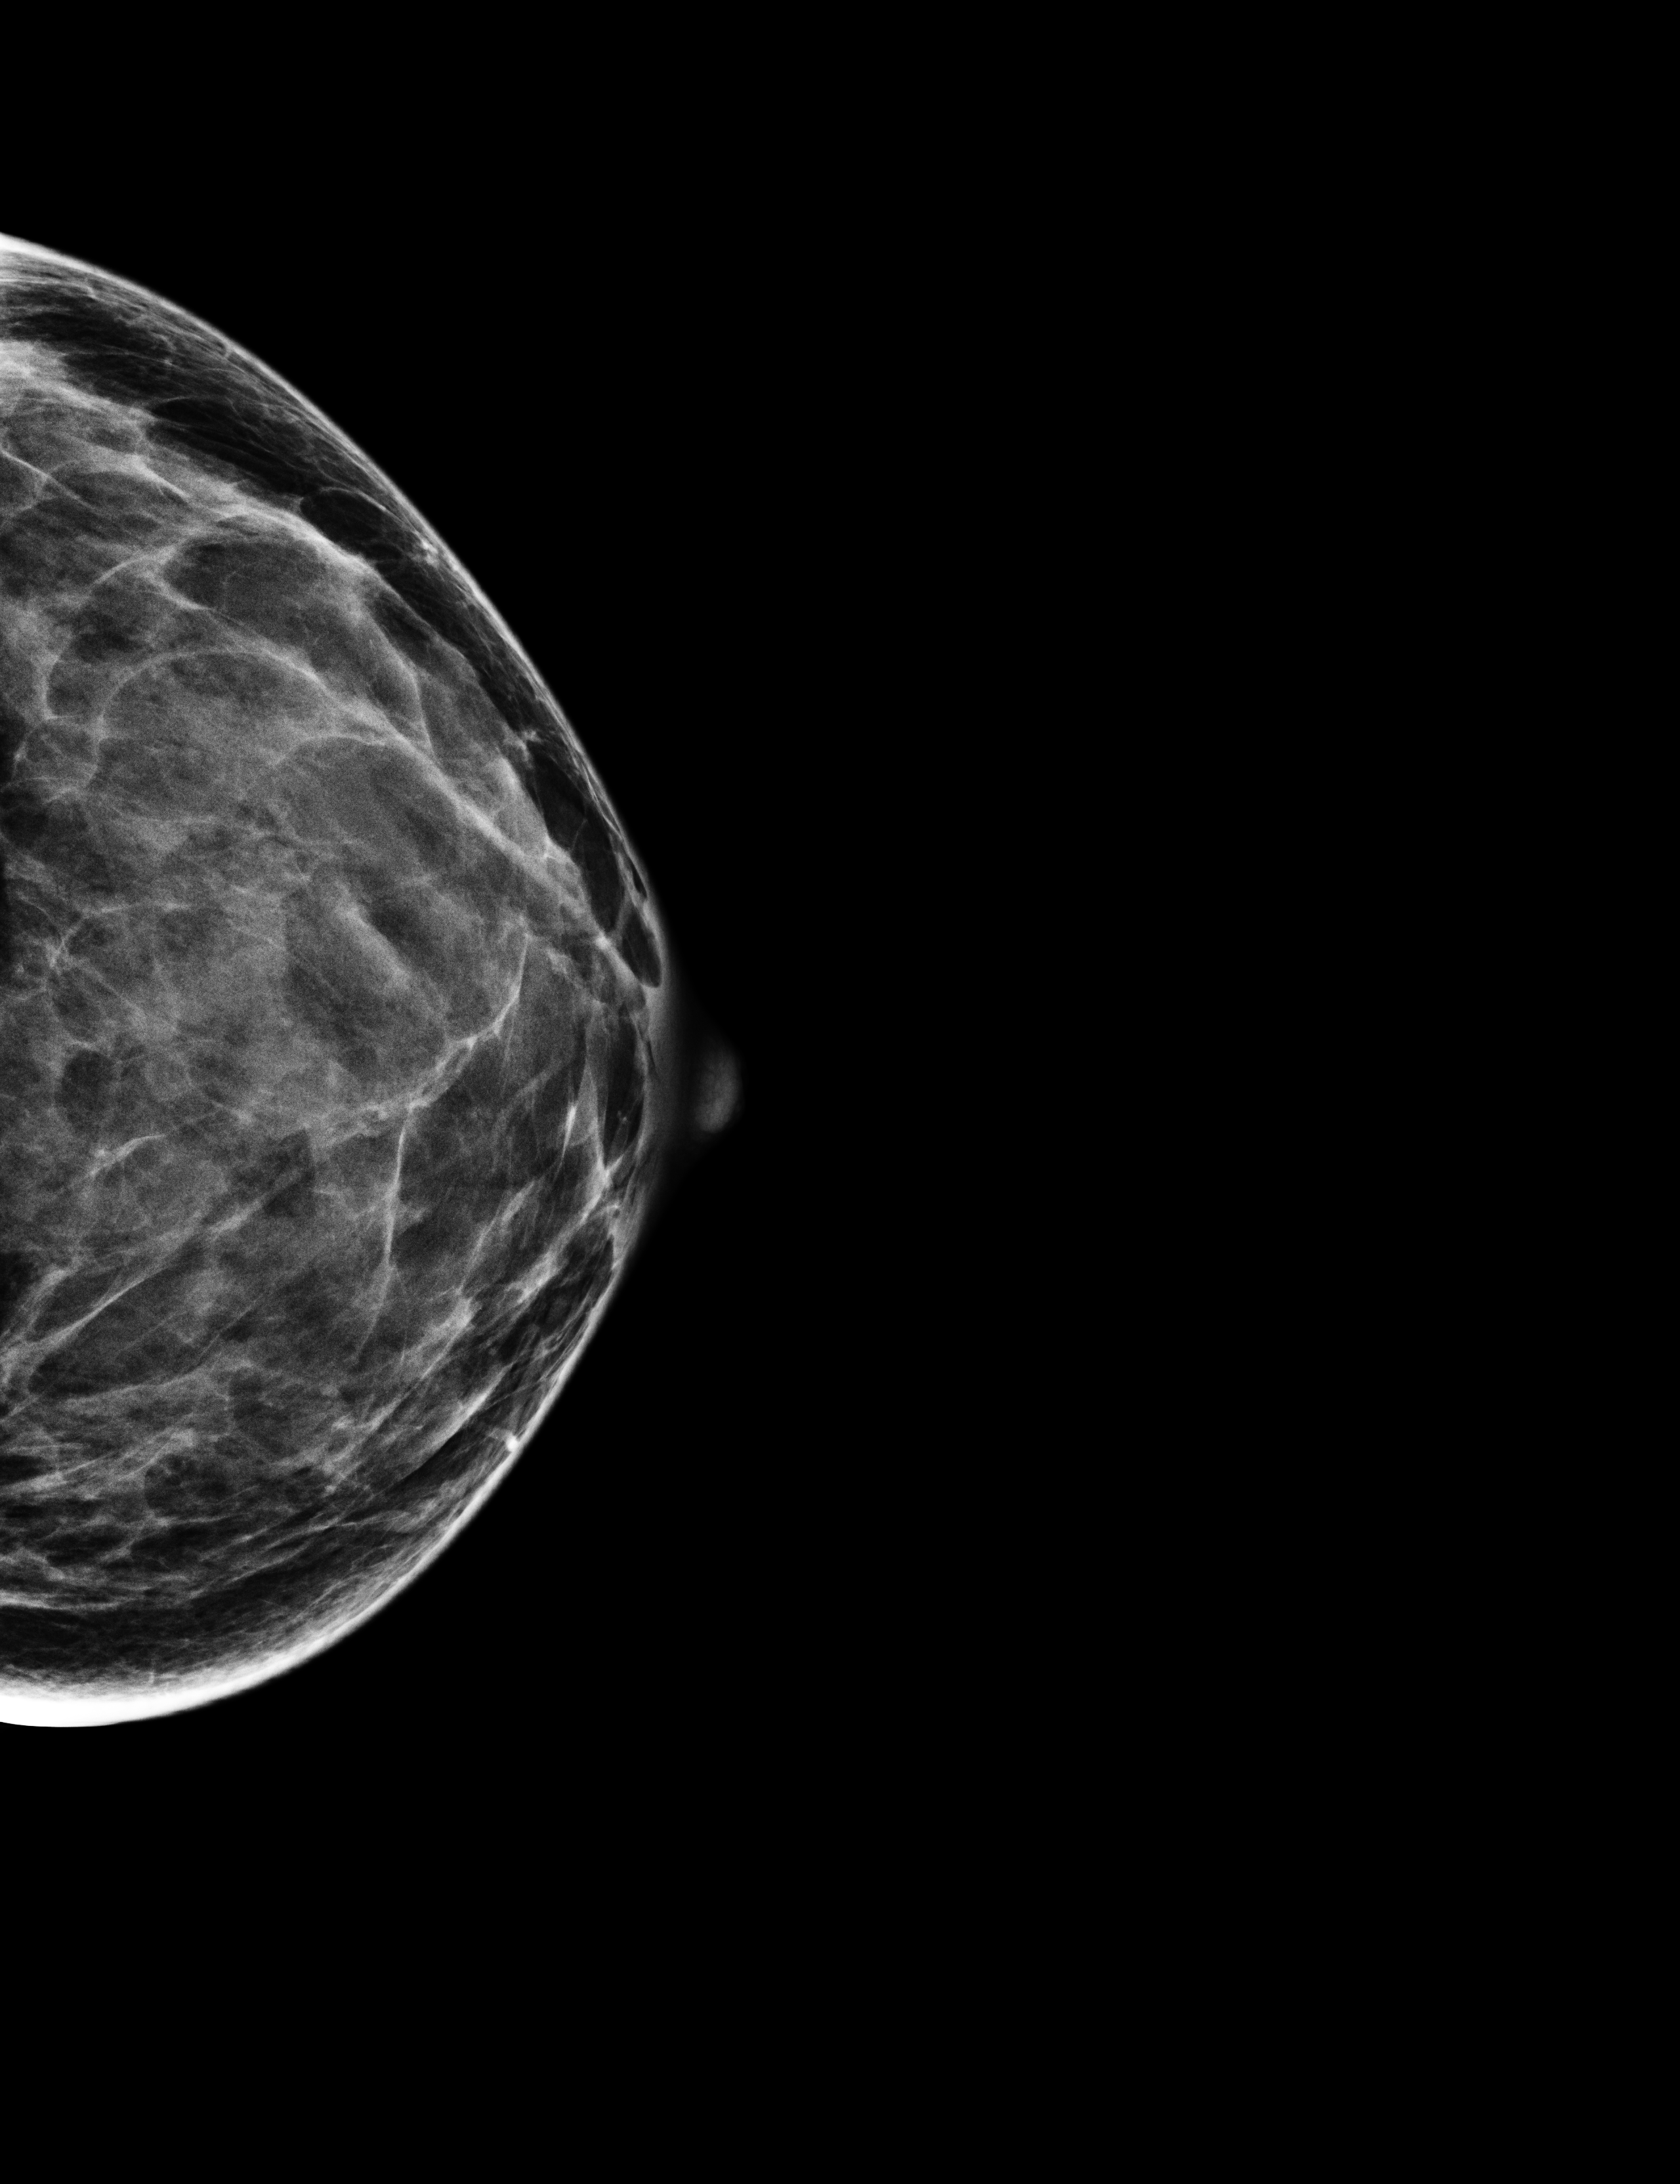
Screening examination. Patient: female, 43 years.
Image type: full-field digital mammogram. Breast: left. Projection: cranio-caudal projection.